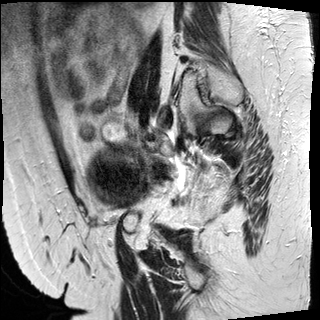
Pelvic MRI for cervical cancer, one sagittal slice; position 16 of 50 along the scan axis; T2-weighted; 1.5 T; TE 89 ms, TR 4880 ms; 4 mm slice thickness; 320 × 320 image matrix. Female patient, age 50 years.
Outlined on this slice (expert manual segmentation):
- uterus and cervix: bounding box (x1, y1, x2, y2) in pixels: (85, 141, 169, 206)